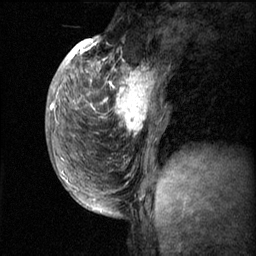
Breast MRI (dynamic contrast-enhanced), one sagittal slice; slice 21 of 60 in the series (ordered by position); dynamic contrast-enhanced series, image 2 of 3 at this slice position (ordered by acquisition); 1.5 T; TE 4.2 ms, TR 11.1 ms; 2 mm slice thickness; 256 × 256 image matrix, field of view 180 × 180 mm. Patient: female, 50 years.
Annotated regions visible in this slice (semi-automatically segmented with operator editing):
- analysis volume of interest (the breast-tissue region the enhancement analysis was run in; not a lesion): box from (x=82, y=56) to (x=168, y=143) px
- tumour enhancement mask (voxels above the 70 % enhancement threshold inside the analysis volume of interest): (x=83, y=58)–(x=155, y=135)